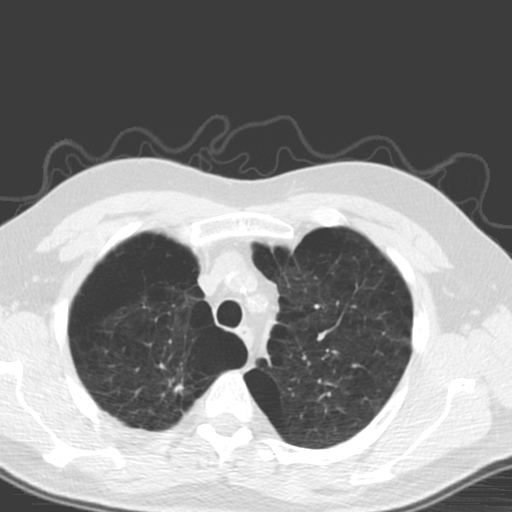
Axial slice from a low-dose chest CT screening exam, baseline annual screen, lung window (W 1500 / L -600 HU), 3.2 mm slice thickness. Male participant, aged 56 years at enrolment. Former smoker at enrolment.
Lesion marked by an expert reader, bounding box <141,353,209,435> (left, top, right, bottom; pixels). The exam's reader record, not a measurement of the box and not confirmed to be the same lesion: non-calcified nodule or mass ≥4 mm, right upper lobe, 20 × 12 mm, spiculated (stellate) margins, soft tissue attenuation. Lung cancer was diagnosed 205 days after this screen: large cell carcinoma, NOS, right upper lobe, poorly differentiated (G3), stage IA (AJCC 6th edition), 18 mm at pathology.